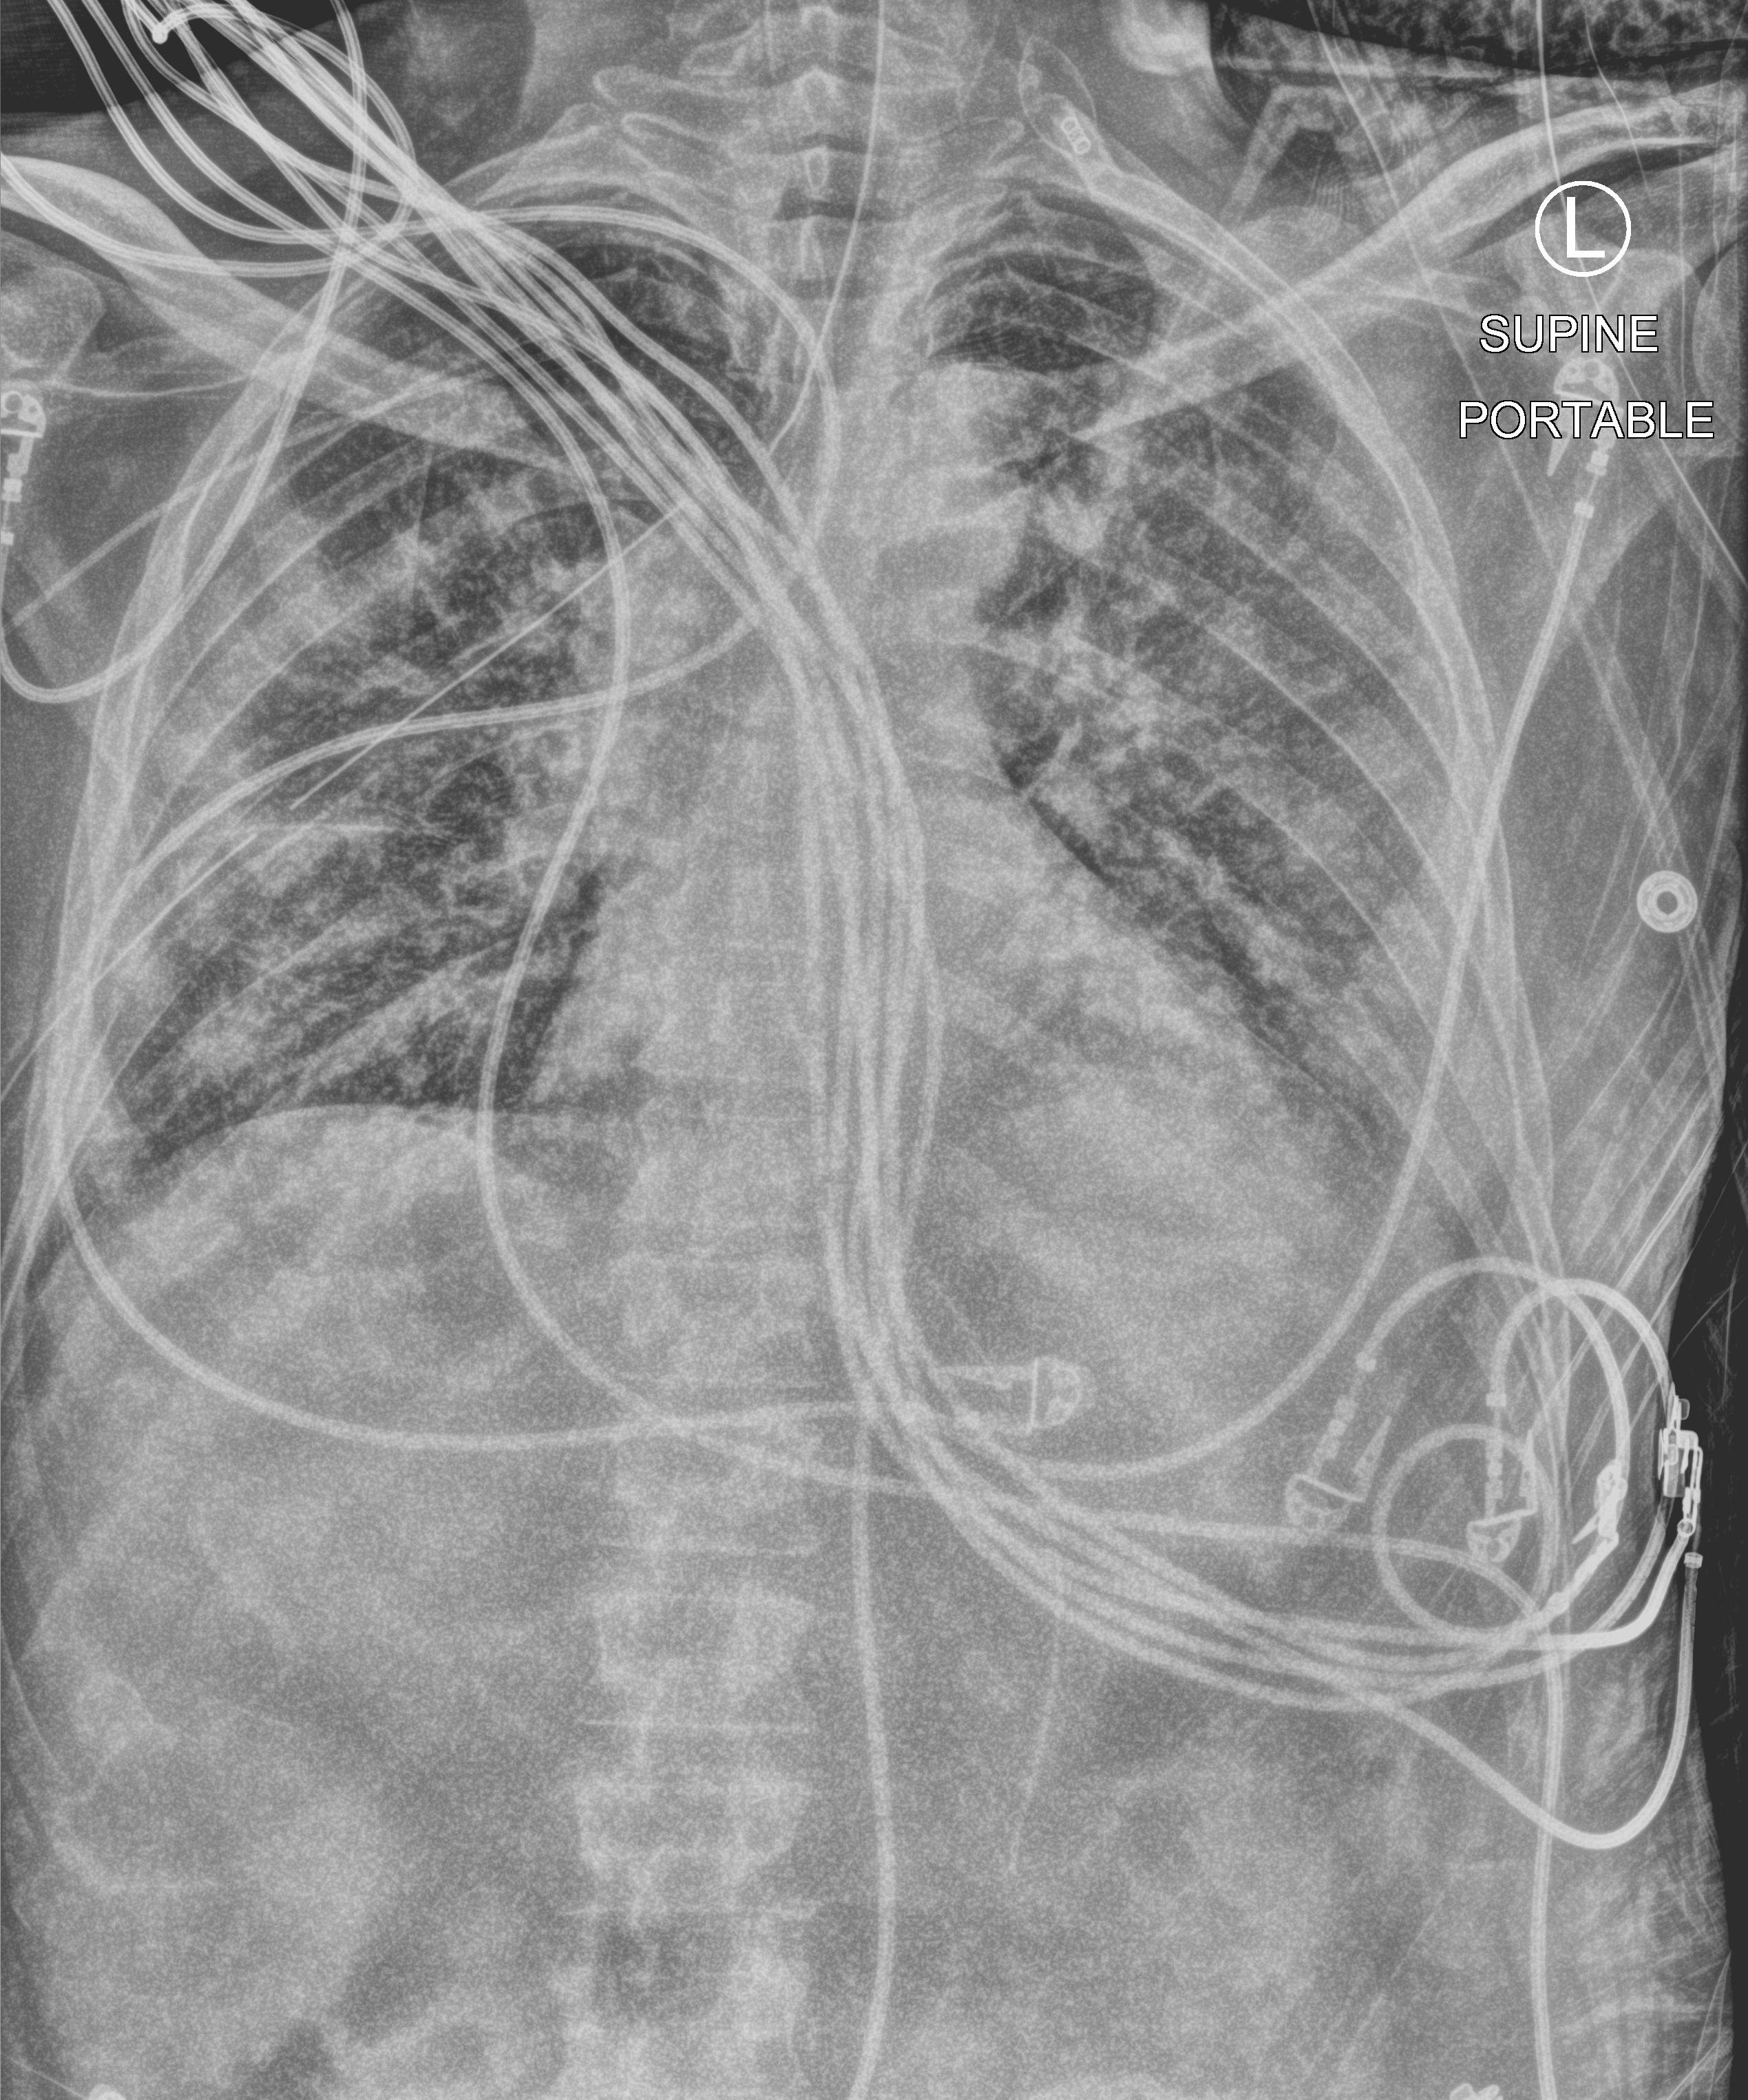
Chest X-ray (portable); anteroposterior (AP) projection. Patient hospitalised with COVID-19; male, aged 18–59 years.
Admission-level facts for this patient (not findings on this image; timing relative to this image not recorded):
- smoking status (admission record): never